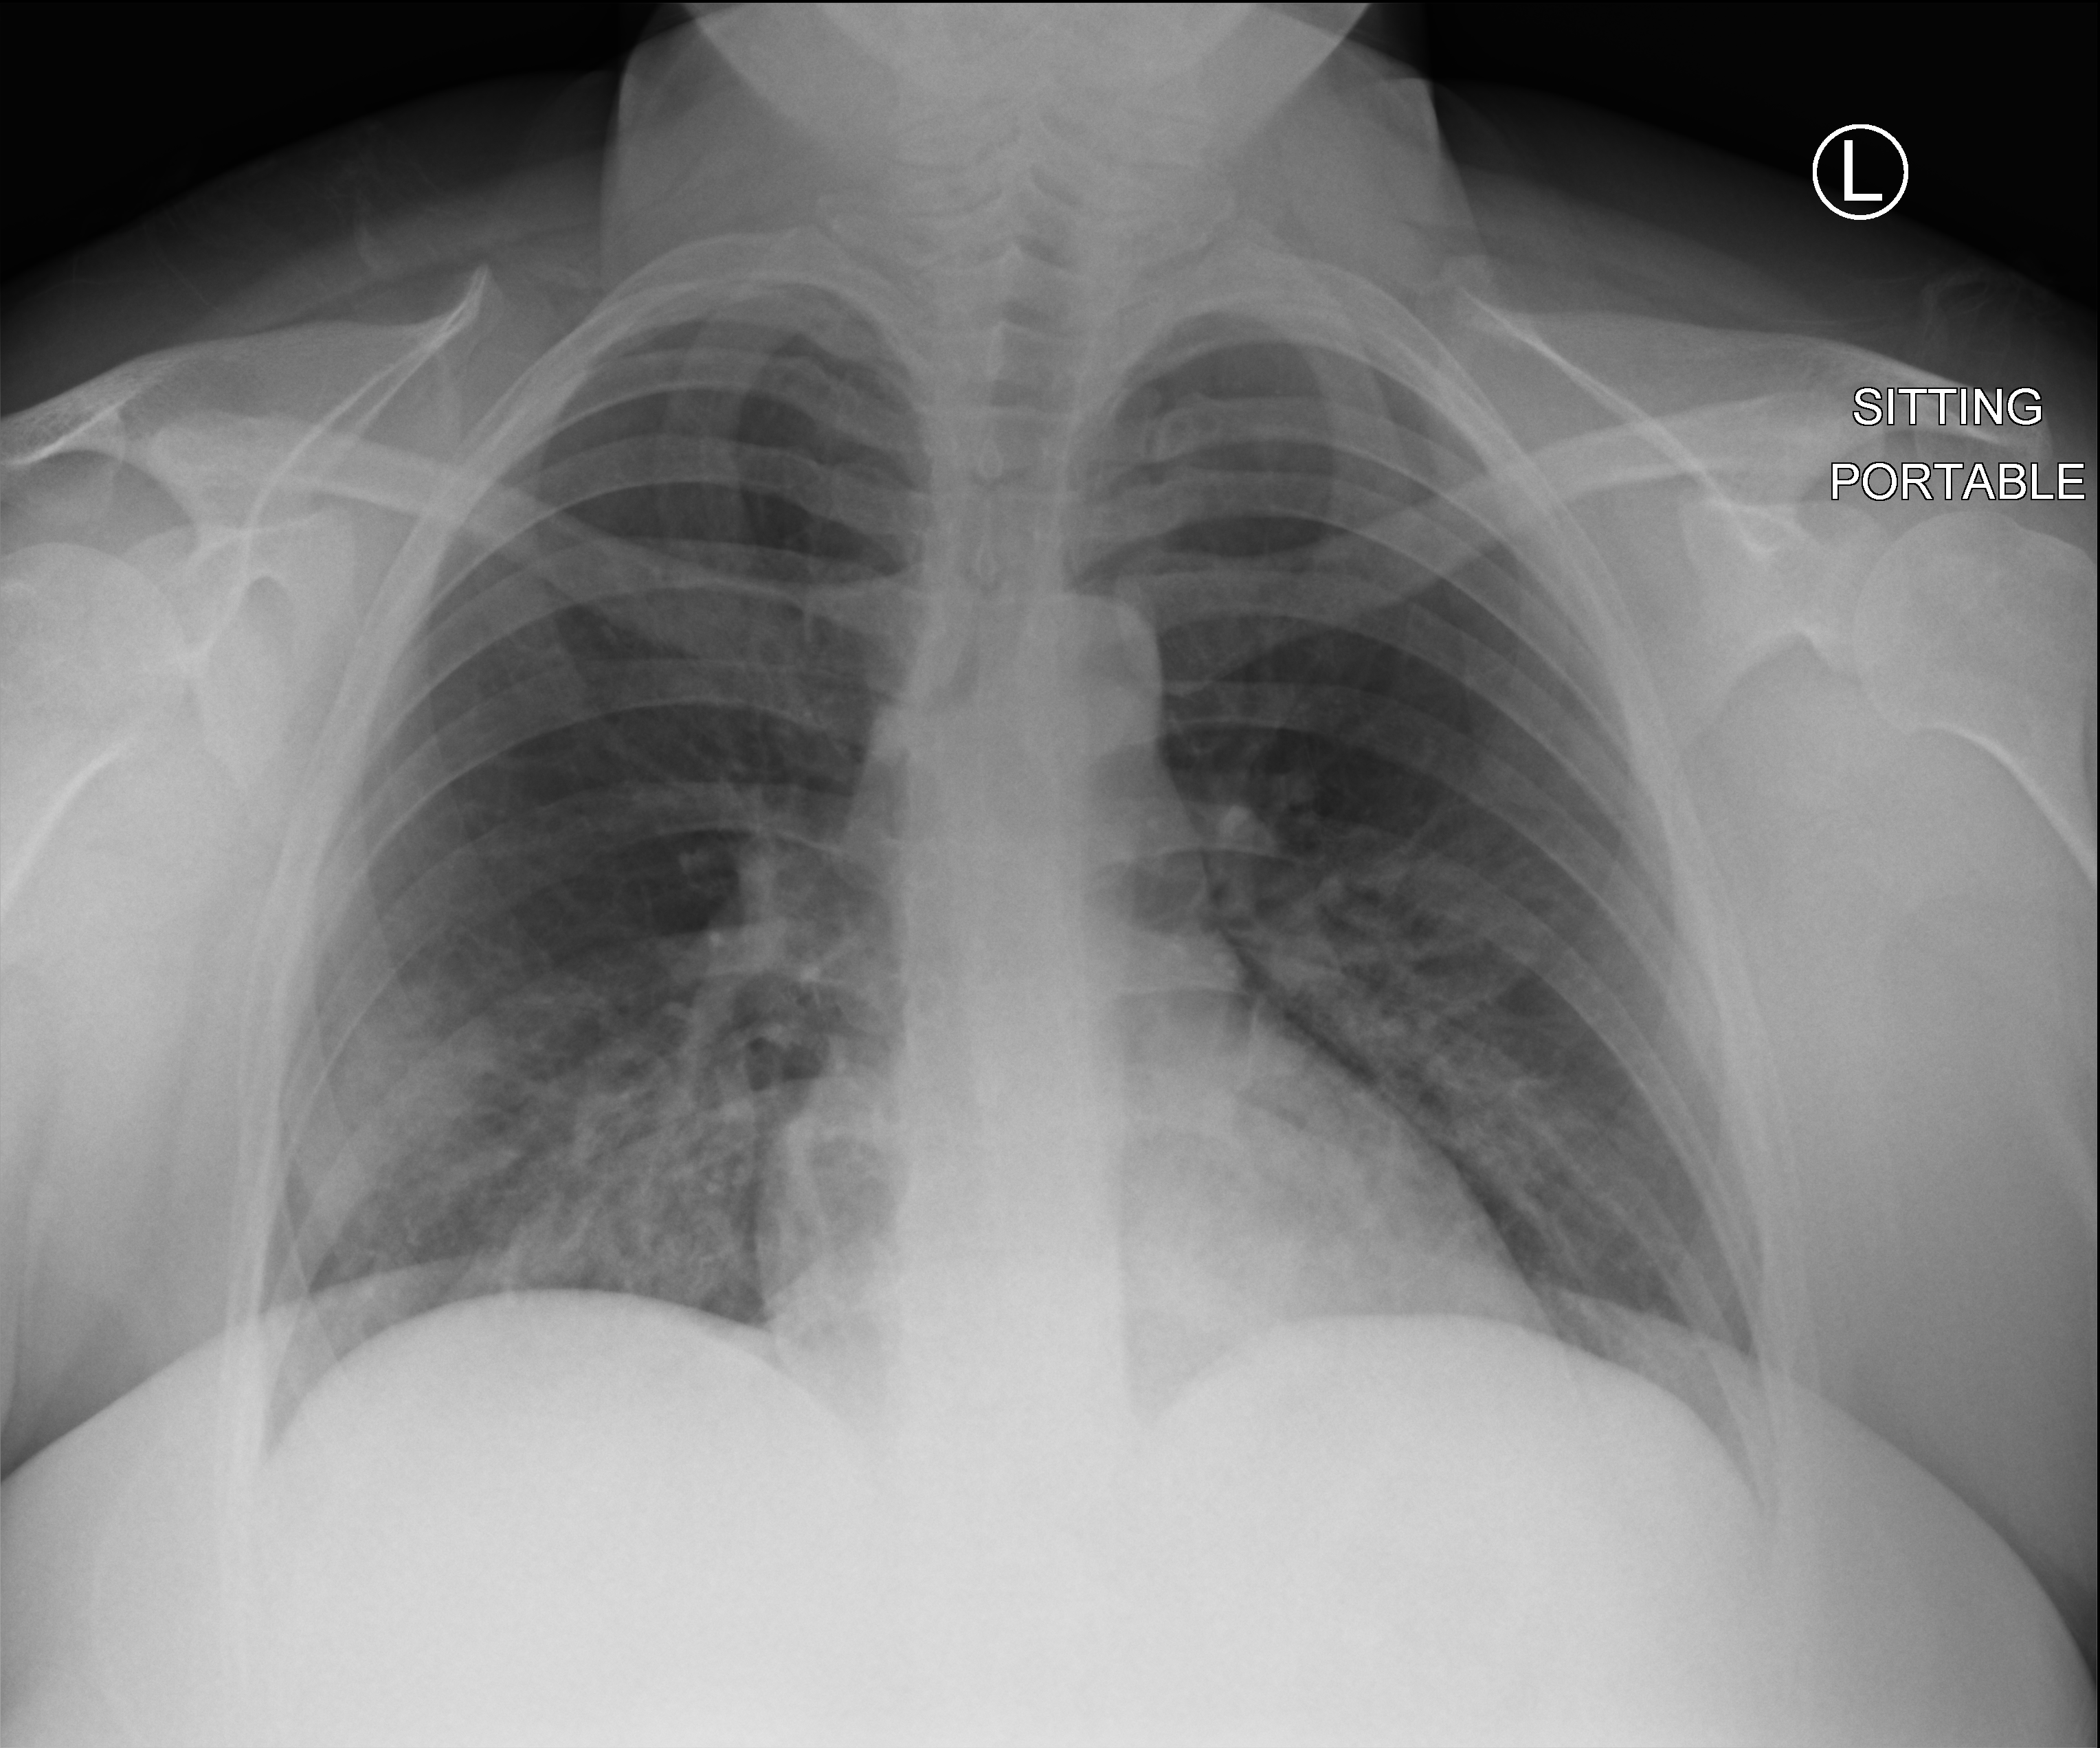
Chest X-ray (portable), anteroposterior (AP) projection. Female patient hospitalised with COVID-19, age 18–59 years.
From the hospital-stay record, not from the radiograph (when in the stay this image was taken is not recorded): admitted to intensive care during this hospital stay: no; mechanically ventilated during this hospital stay: no; COPD (admission record): no.